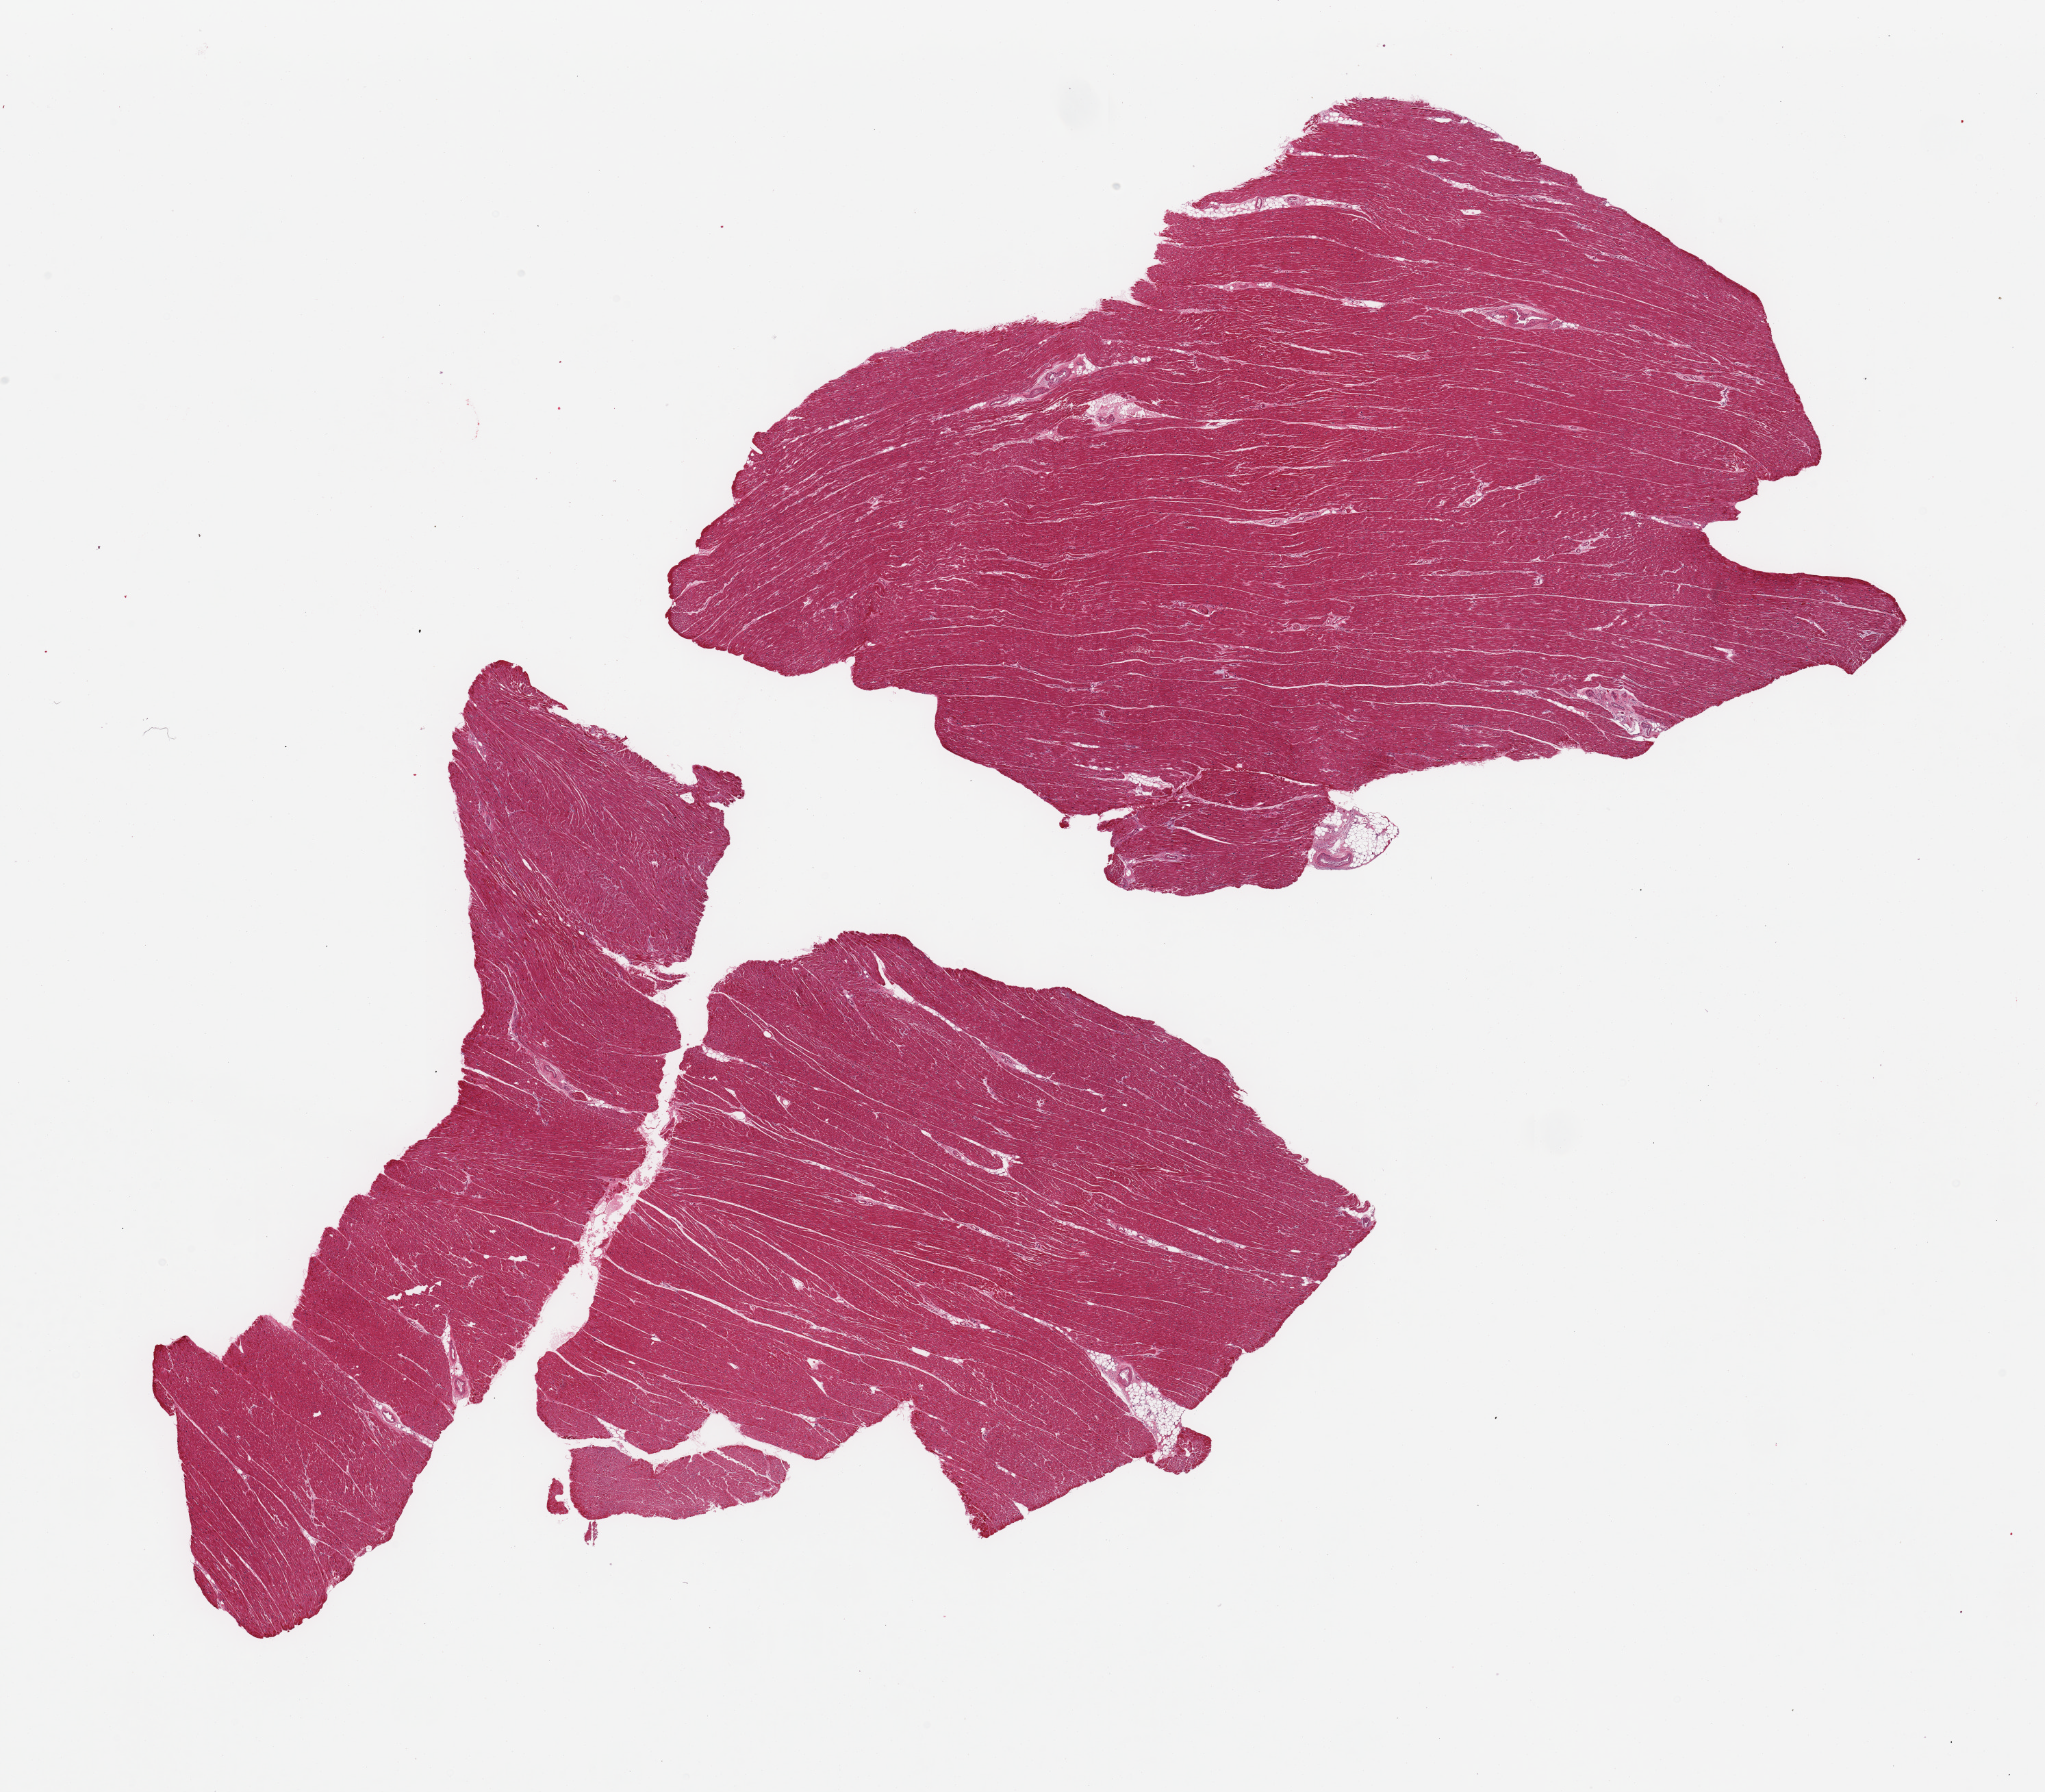
Haematoxylin and eosin whole-slide image — shown as a low-resolution overview of the whole scanned area (about 23.6 x 20.7 mm, acquisition: 20x scan); PAXgene-fixed, paraffin-embedded tissue; target tissue: heart; tissue donor sample. Donor: female.
Pathologist's review note for this sample: 2 pieces, minimal interstitial fibrosis; subacute/agonal ischemic changes (contraction bands) prominent.